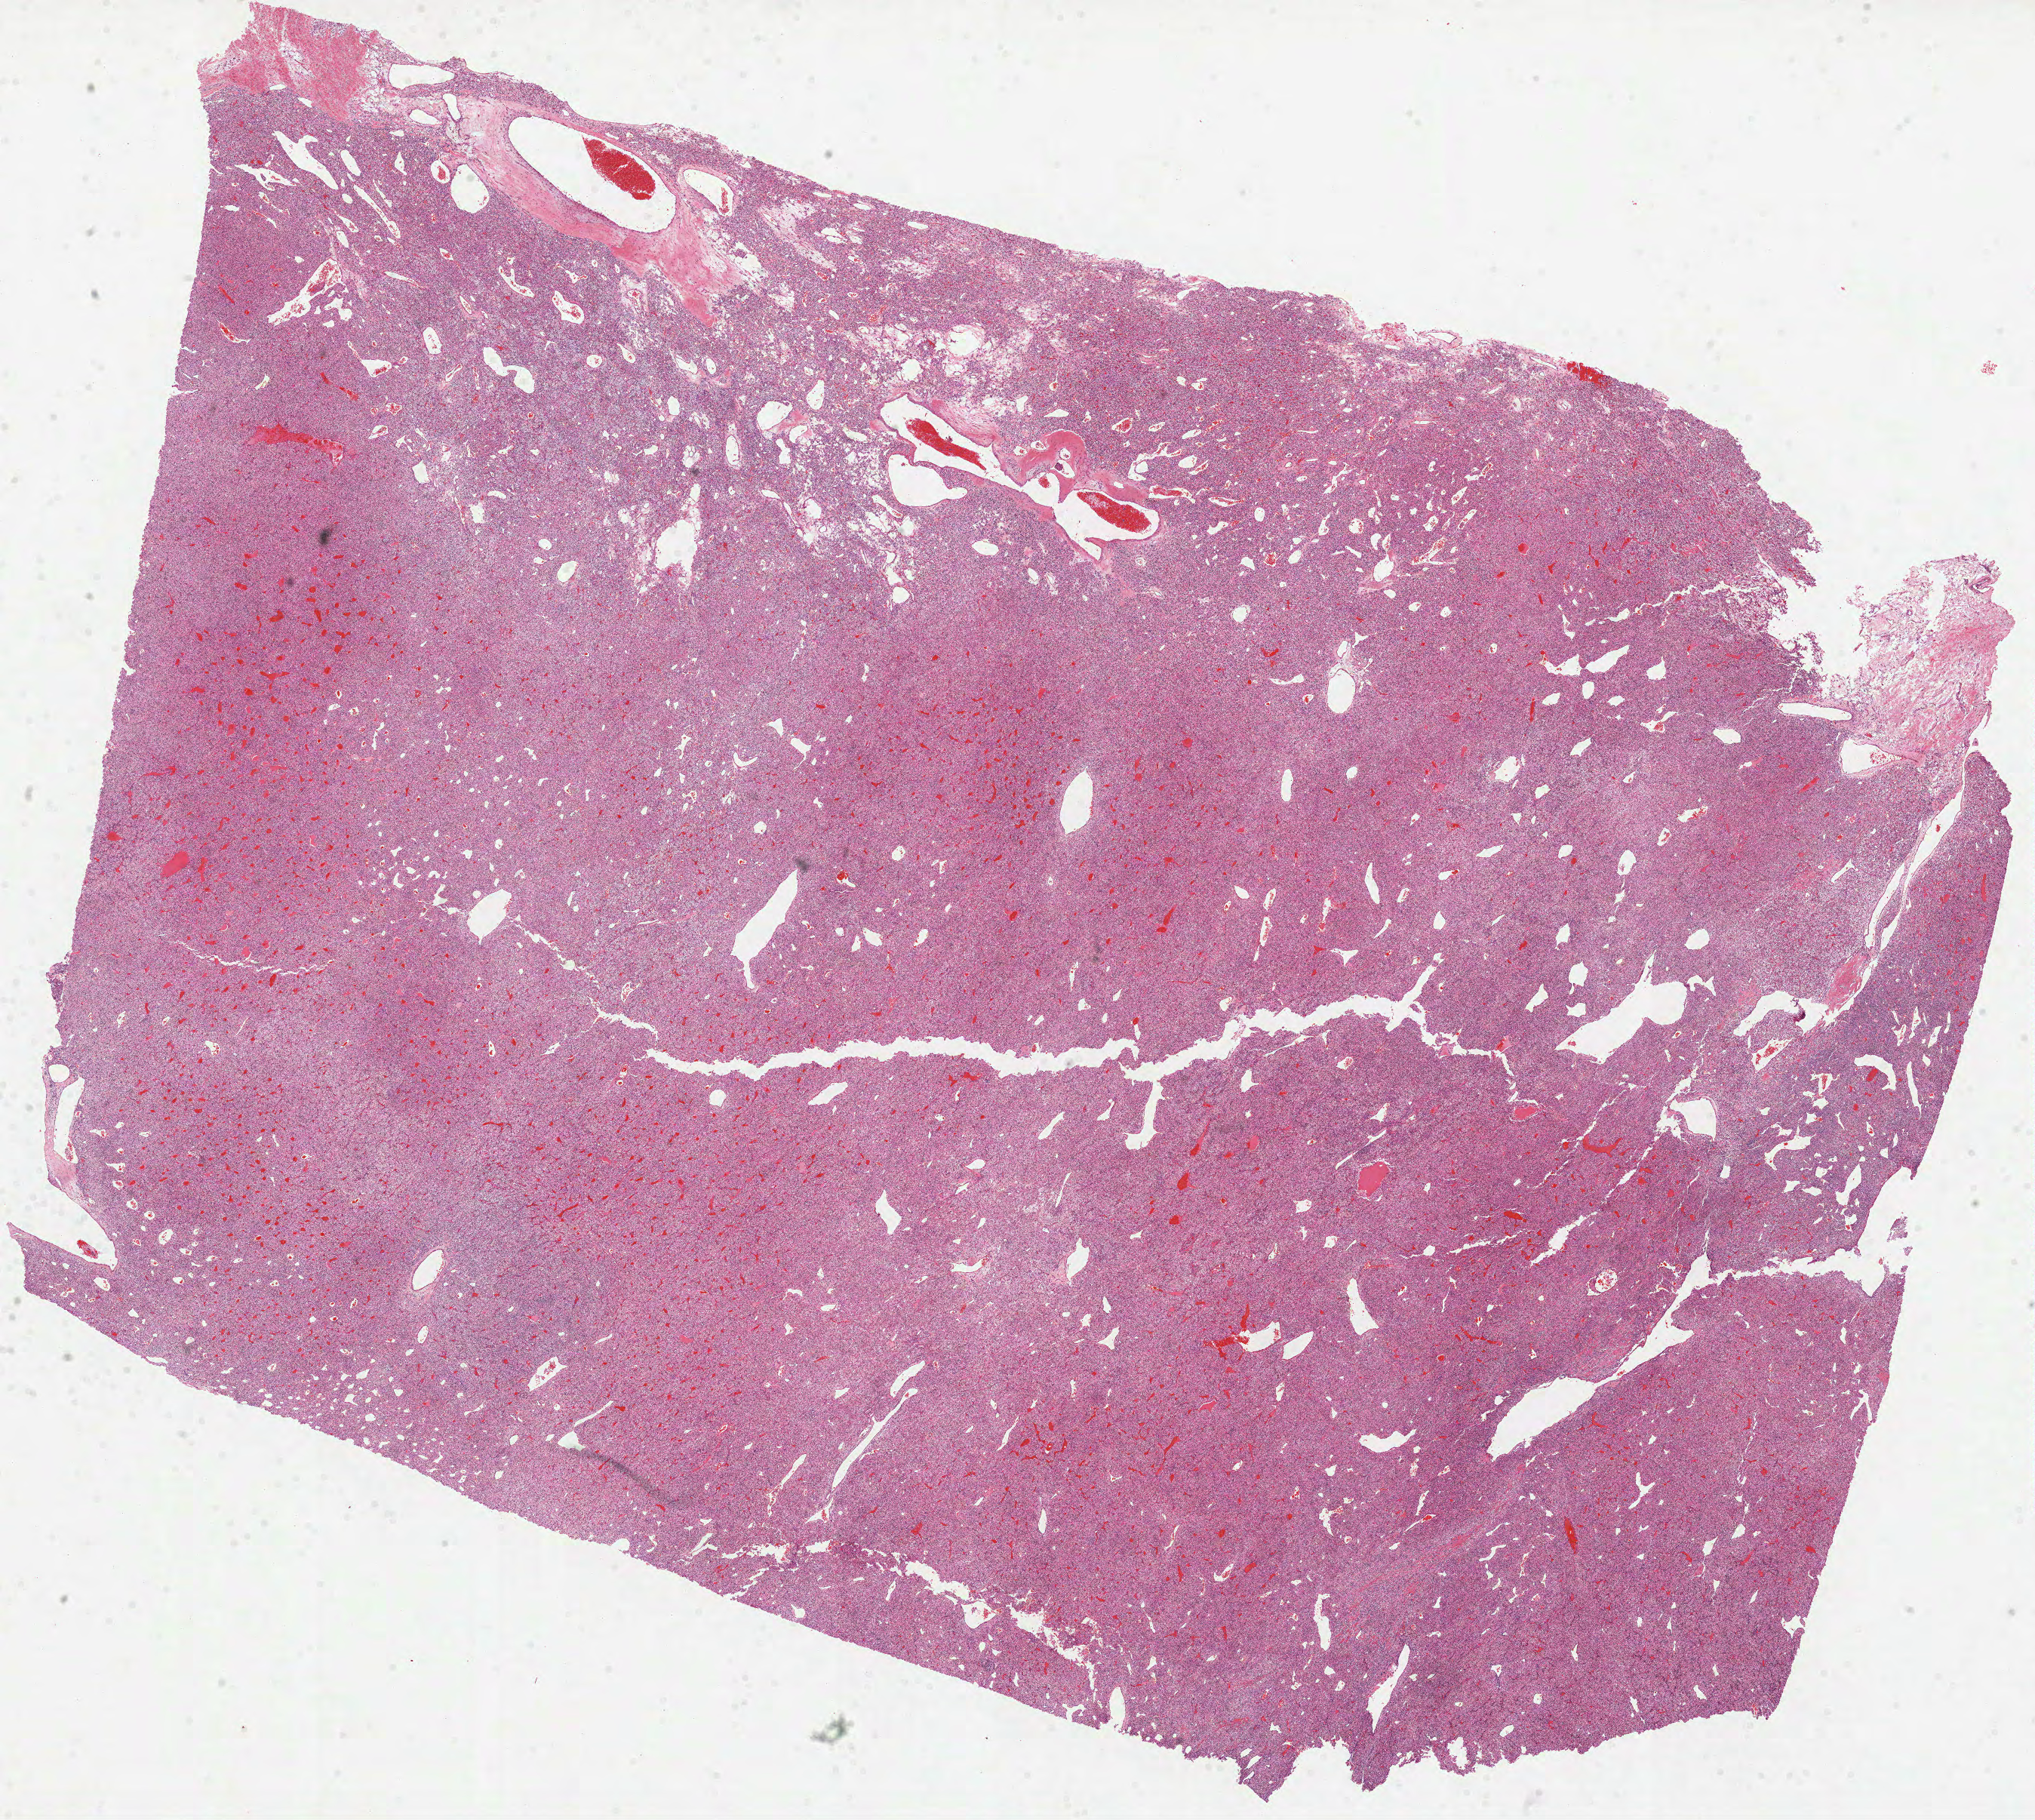
Whole-slide histology image, H&E — whole scanned area (about 21.8 x 19.5 mm) shown as a low-resolution overview; formalin-fixed paraffin-embedded (FFPE) diagnostic section; primary tumour sample from the kidney. Male, age 57 years at initial diagnosis.
Histologic diagnosis: Clear cell adenocarcinoma, NOS.